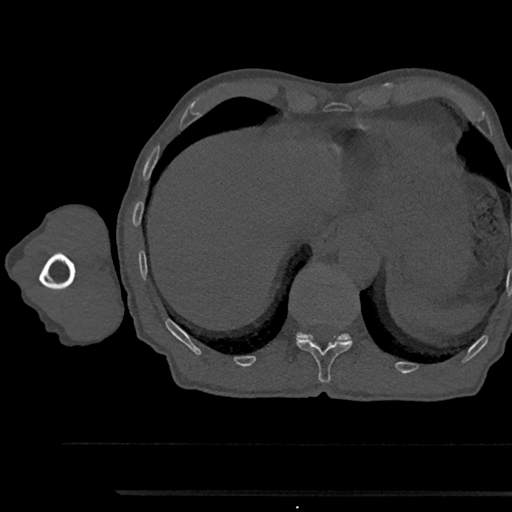
CT including the spine, one axial slice; slice 763 of 797 in the series (ordered by position); reconstruction kernel Br40s/3; 120 kVp; bone window (W 1800 / L 400 HU); 512 × 512 image matrix, field of view 367 × 367 mm. Patient: male, 79 years. From the clinical record (not read from this slice): primary cancer: prostate.
Outlined on this slice (semi-automatic segmentation, software-assisted and operator-edited):
- T11 vertebra: bounding box <296,338,352,383> (left, top, right, bottom; pixels)
- T12 vertebra: <296,265,352,342>